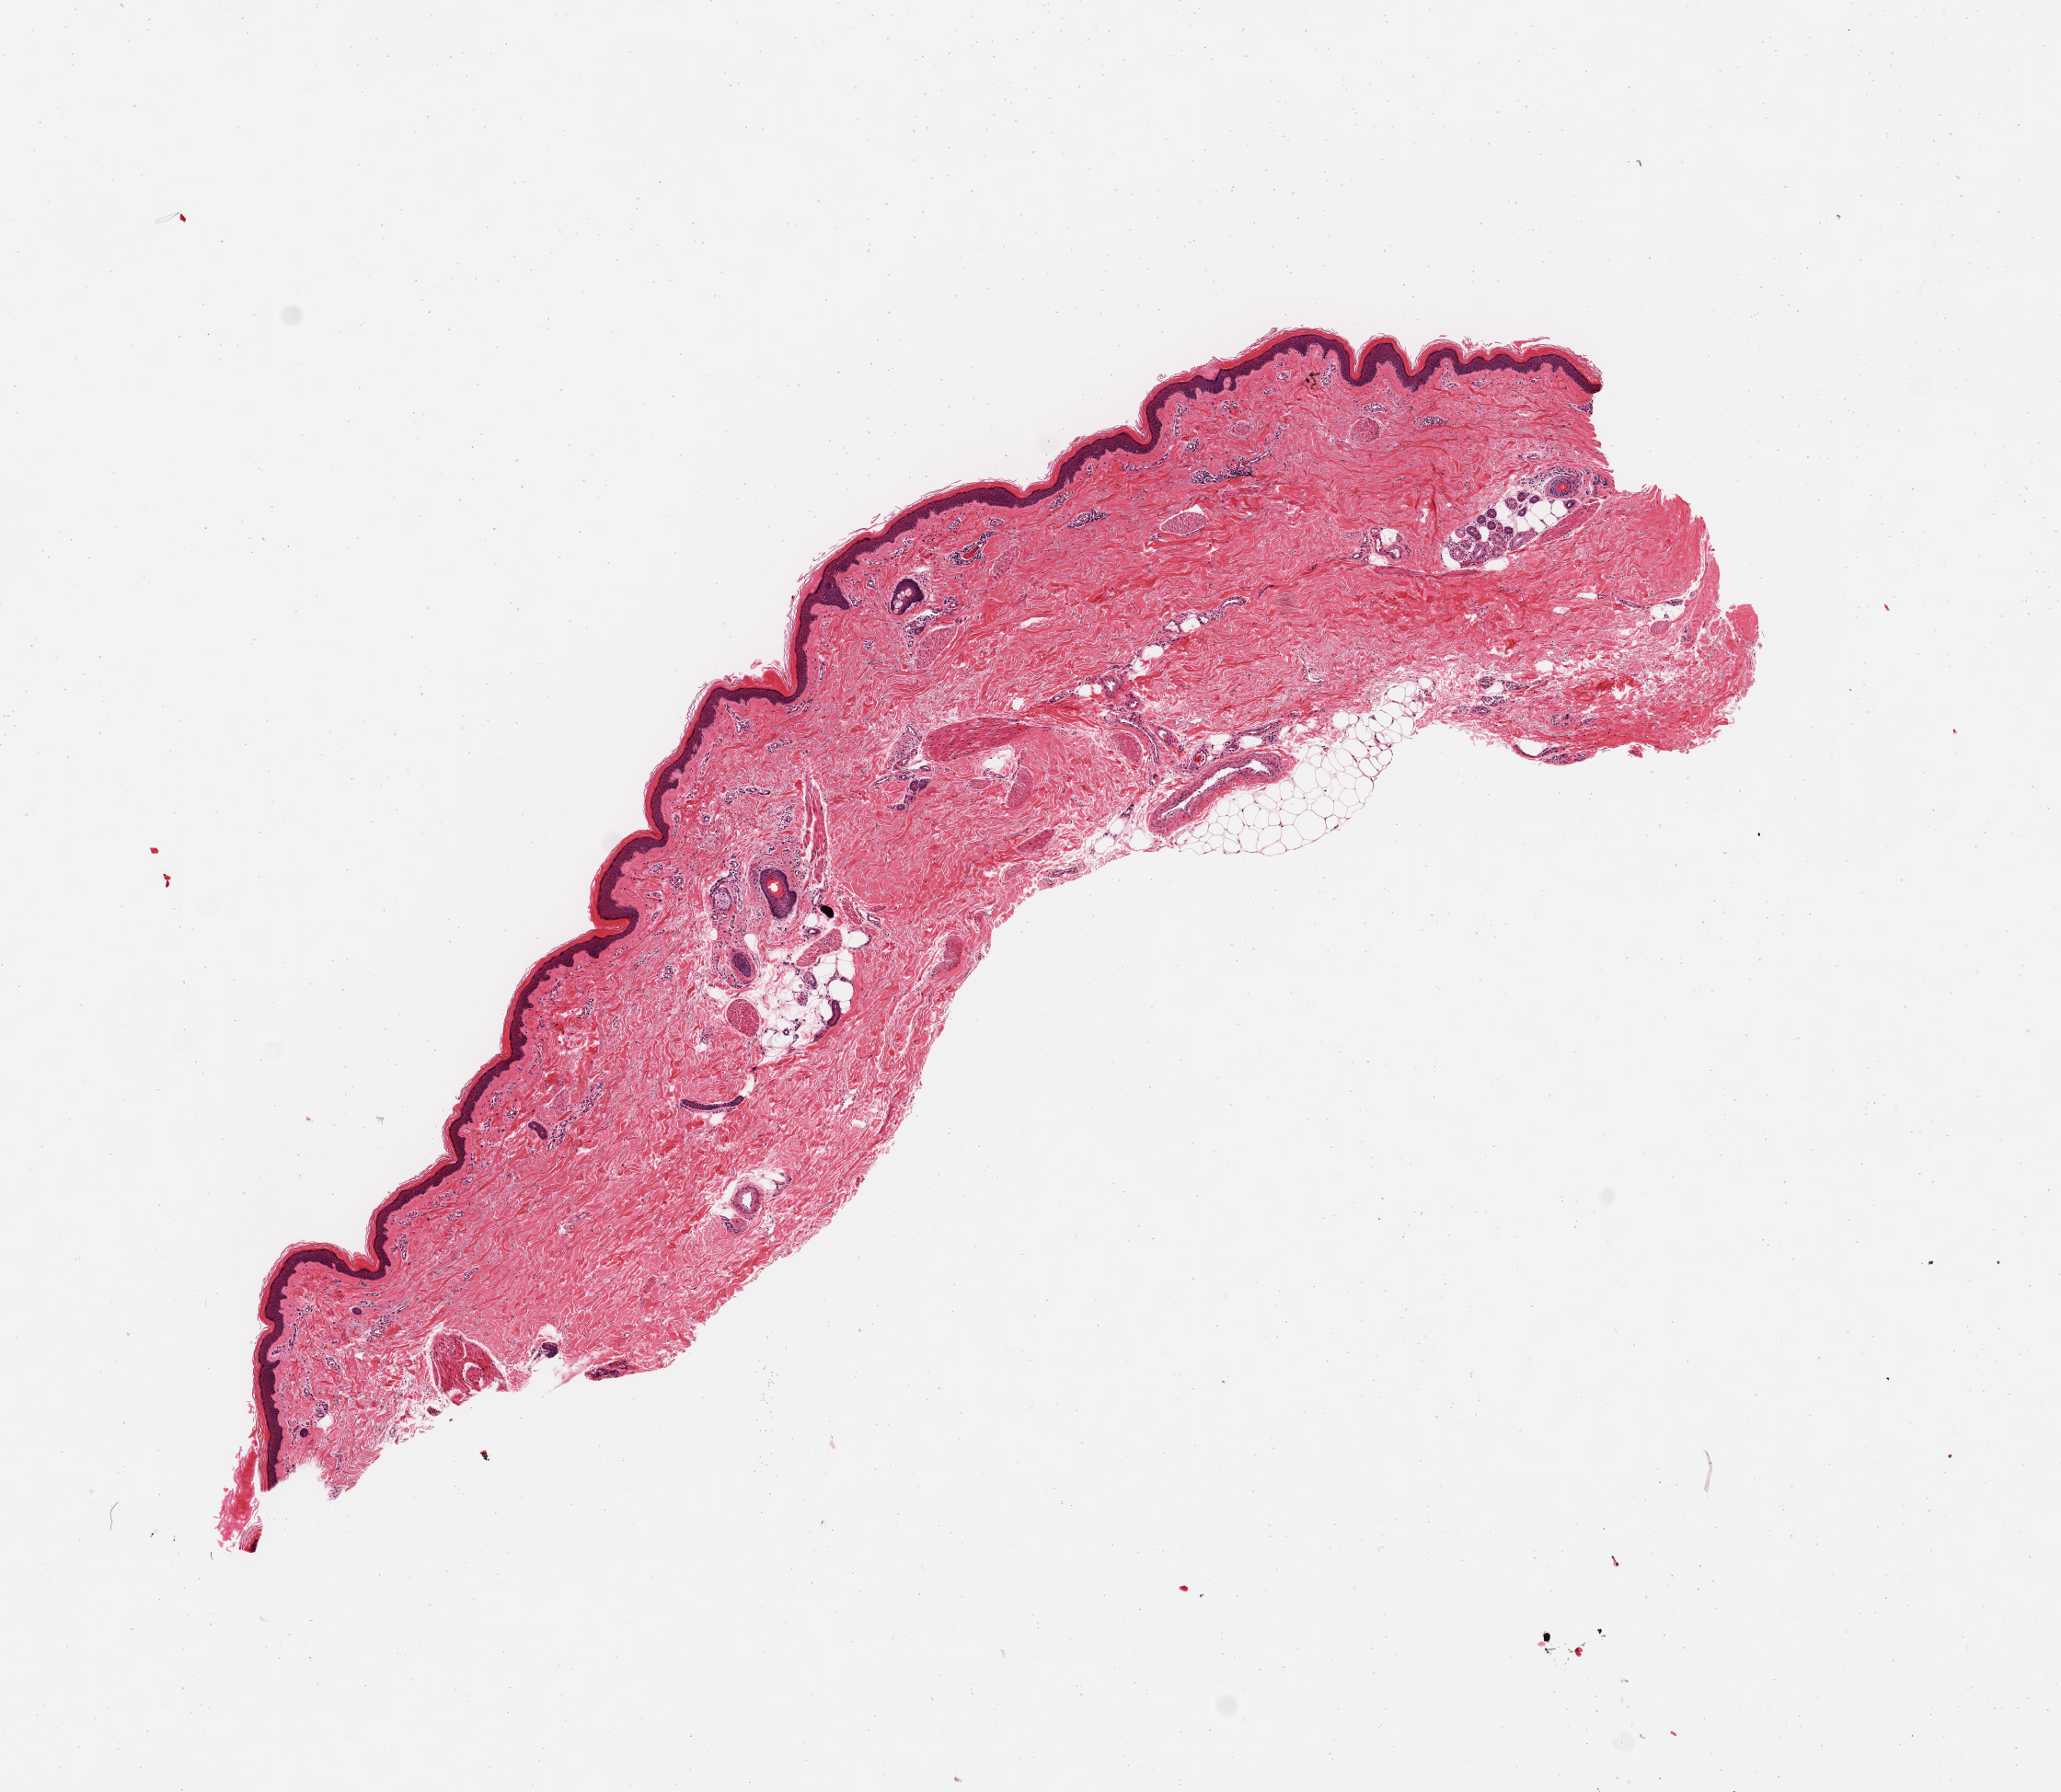
Digitized haematoxylin and eosin-stained section, shown as a low-resolution overview of the whole scanned area (about 8.9 x 7.7 mm, from a 20x scan); PAXgene-fixed paraffin-embedded (PFPE) section; sampled site (target tissue): skin of lower leg; donor tissue sample. Donor: female.
Review note (as recorded): 1 piece skin, as with 2625.